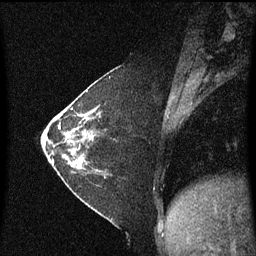
Breast MRI (dynamic contrast-enhanced), one sagittal slice. Slice 22 of 60 in the series (ordered by position). Dynamic contrast-enhanced series, image 2 of 3 at this slice position (ordered by acquisition). 1.5 T. TE 4.2 ms, TR 8.4 ms. 2 mm slice thickness. 256 × 256 image matrix, field of view 200 × 200 mm. Patient: female, 36 years. Case-level facts recorded for this patient, not image findings: setting: breast cancer imaged before/during neoadjuvant chemotherapy; receptor status: HR-positive, HER2-negative.
Outlined on this slice (semi-automatic segmentation, software-assisted and operator-edited):
- analysis volume of interest (the breast-tissue region the enhancement analysis was run in; not a lesion): bounding box [x1, y1, x2, y2] px = [66, 102, 110, 179]
- tumour enhancement mask (voxels above the 70 % enhancement threshold inside the analysis volume of interest): [85, 110, 96, 133]